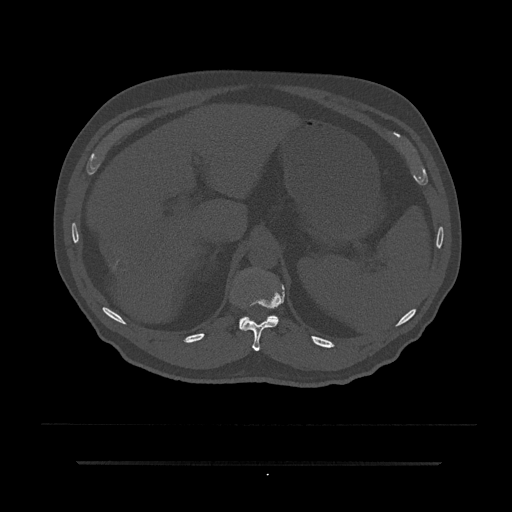
CT including the spine, one axial slice; slice 246 of 797 in the series (ordered by position); reconstruction kernel Br40s/3; 120 kVp; bone window (W 1800 / L 400 HU); 512 × 512 image matrix, field of view 464 × 464 mm. Patient: male, 59 years. Case-level facts recorded for this patient, not image findings: primary cancer: bile ducts; vertebrae with lytic lesions (as recorded): T10.
Annotated regions visible in this slice (semi-automatically segmented with operator editing):
- T11 vertebra: box from (x=241, y=285) to (x=284, y=351) px
- T12 vertebra: (x=239, y=315)–(x=279, y=331)